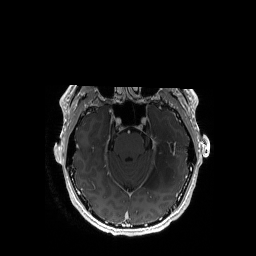
Brain MRI from a brain-tumour surgery series, one axial slice. Position 119 of 192 along the scan axis. T1-weighted post-contrast. 256 × 256 image matrix, field of view 256 × 256 mm. From the clinical record (not read from this slice): histopathology: Astrocytoma; WHO grade: 3; IDH mutation: yes; tumour location: Left Temporal.
Outlined on this slice (outlined manually by an expert reader):
- tumour: bounding box <145,116,177,189> (left, top, right, bottom; pixels)